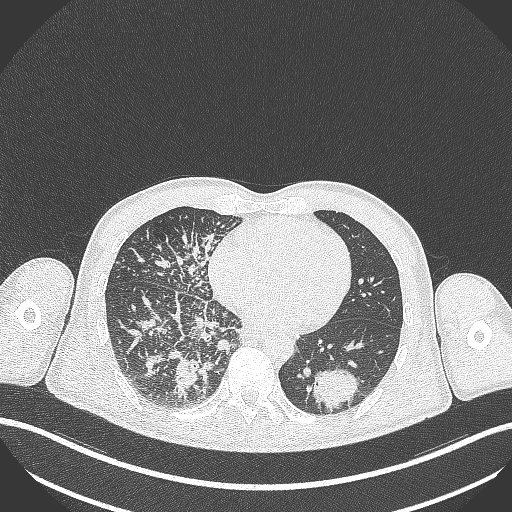
Chest CT, one axial slice. Slice 114 of 348 in the series (ordered by position). Reconstruction kernel B70f. Lung window (W 1500 / L -600 HU). 1 mm slice thickness. 512 × 512 image matrix, field of view 400 × 400 mm. Male patient, age 49 years. Case-level facts recorded for this patient, not image findings: clinical TNM (as recorded): T2b N1 M0.
Structures marked on this image (bounding box drawn by a radiologist):
- lung tumour (recorded histology: adenocarcinoma): bounding box [x1, y1, x2, y2] px = [305, 364, 364, 412]